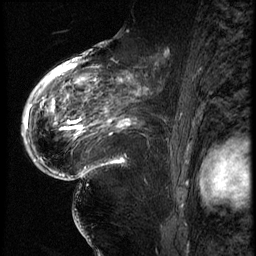
Breast MRI (dynamic contrast-enhanced), one sagittal slice; position 40 of 62 along the scan axis; 3 images stored at this slice position (order not interpretable as contrast timing); 1.5 T; TE 4.2 ms, TR 9 ms; 2.5 mm slice thickness; 256 × 256 image matrix, field of view 180 × 180 mm. Patient: female, 56 years. Case-level facts recorded for this patient, not image findings: setting: breast cancer imaged before/during neoadjuvant chemotherapy; receptor status: HER2-positive.
Structures marked on this image (semi-automatically segmented with operator editing):
- analysis volume of interest (the breast-tissue region the enhancement analysis was run in; not a lesion): box from (x=84, y=75) to (x=181, y=153) px
- tumour enhancement mask (voxels above the 140 % enhancement threshold inside the analysis volume of interest): (x=84, y=75)–(x=133, y=137)